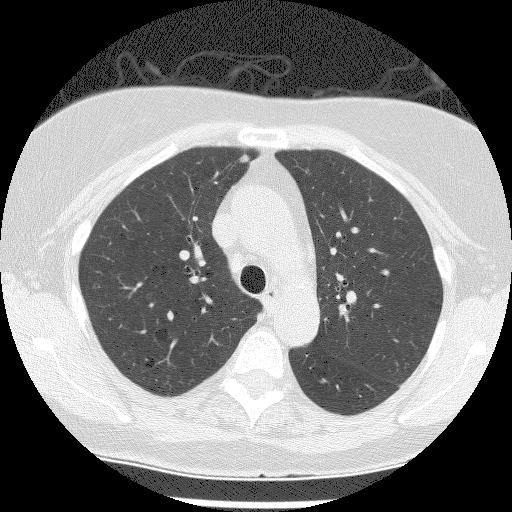
Low-dose screening chest CT, axial slice. Second annual screen. Lung window (W 1500 / L -600 HU). 2.5 mm slice thickness. Lung (sharp) reconstruction kernel (BONE). Slice 46 of 149 in the series. Female, age 61 years at enrolment. Current smoker at enrolment.
Lesion marked by an expert reader, bounding box [x1, y1, x2, y2] px = [226, 144, 256, 171]. Reader record for this screening exam (exam-level; its link to the box is not recorded): non-calcified nodule or mass ≥4 mm, right upper lobe, 5 × 4 mm, smooth margins, soft tissue attenuation, pre-existing on the prior screen: no. Participant outcome: lung cancer diagnosed 244 days after this screen — adenocarcinoma, NOS, right upper lobe, moderately differentiated (G2), stage IA (AJCC 6th edition), 8 mm at pathology.